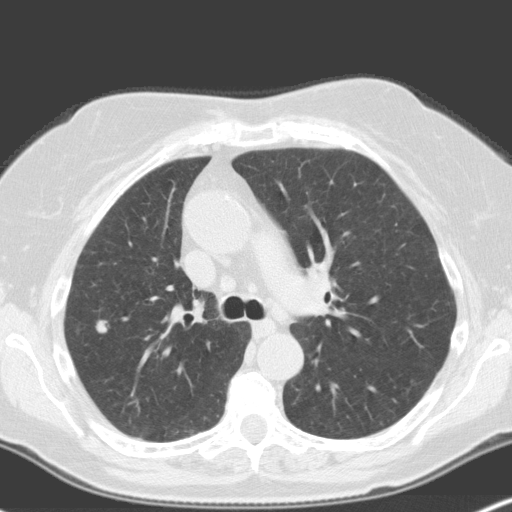
Low-dose screening chest CT, one axial slice. Position 114 of 160 along the scan axis. Lung window (W 1500 / L -600 HU). 512 × 512 image matrix, field of view 316 × 316 mm.
Annotated regions visible in this slice (outlined manually by an expert reader):
- lesion 3 (nodule): bounding box (x1, y1, x2, y2) in pixels: (95, 320, 109, 334)